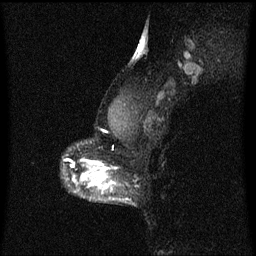
Breast MRI (dynamic contrast-enhanced), one sagittal slice. Position 46 of 60 along the scan axis. Dynamic contrast-enhanced series, image 2 of 3 at this slice position (ordered by acquisition). 1.5 T. TE 4.2 ms, TR 8.4 ms. 2 mm slice thickness. 256 × 256 image matrix, field of view 200 × 200 mm. Patient: female, 40 years.
Outlined on this slice (semi-automatically segmented with operator editing):
- analysis volume of interest (the breast-tissue region the enhancement analysis was run in; not a lesion): bounding box (x1, y1, x2, y2) in pixels: (76, 172, 122, 201)
- tumour enhancement mask (voxels above the 70 % enhancement threshold inside the analysis volume of interest): (82, 172, 115, 189)